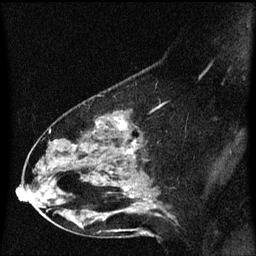
Breast MRI (dynamic contrast-enhanced), one sagittal slice; dynamic contrast-enhanced series, image 2 of 3 at this slice position (ordered by acquisition); 1.5 T; TE 4.2 ms, TR 8.4 ms; 2 mm slice thickness; 256 × 256 image matrix, field of view 200 × 200 mm. Female patient, age 49 years. From the clinical record (not read from this slice): setting: breast cancer imaged before/during neoadjuvant chemotherapy; receptor status: HR-positive, HER2-negative.
Outlined on this slice (semi-automatic segmentation, software-assisted and operator-edited):
- analysis volume of interest (the breast-tissue region the enhancement analysis was run in; not a lesion): bounding box [x1, y1, x2, y2] px = [27, 100, 170, 221]
- tumour enhancement mask (voxels above the 70 % enhancement threshold inside the analysis volume of interest): [117, 118, 134, 197]